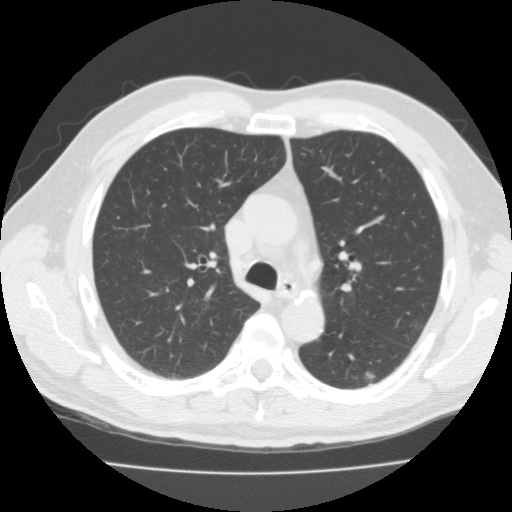
Low-dose screening chest CT, one axial slice. Position 68 of 99 along the scan axis. Reconstruction kernel FC02. 120 kVp. Lung window (W 1500 / L -600 HU). 512 × 512 image matrix, field of view 359 × 359 mm.
Annotated regions visible in this slice (expert manual segmentation):
- lesion 1 (tumor, lower lobe of left lung): bounding box [x1, y1, x2, y2] px = [366, 372, 375, 379]